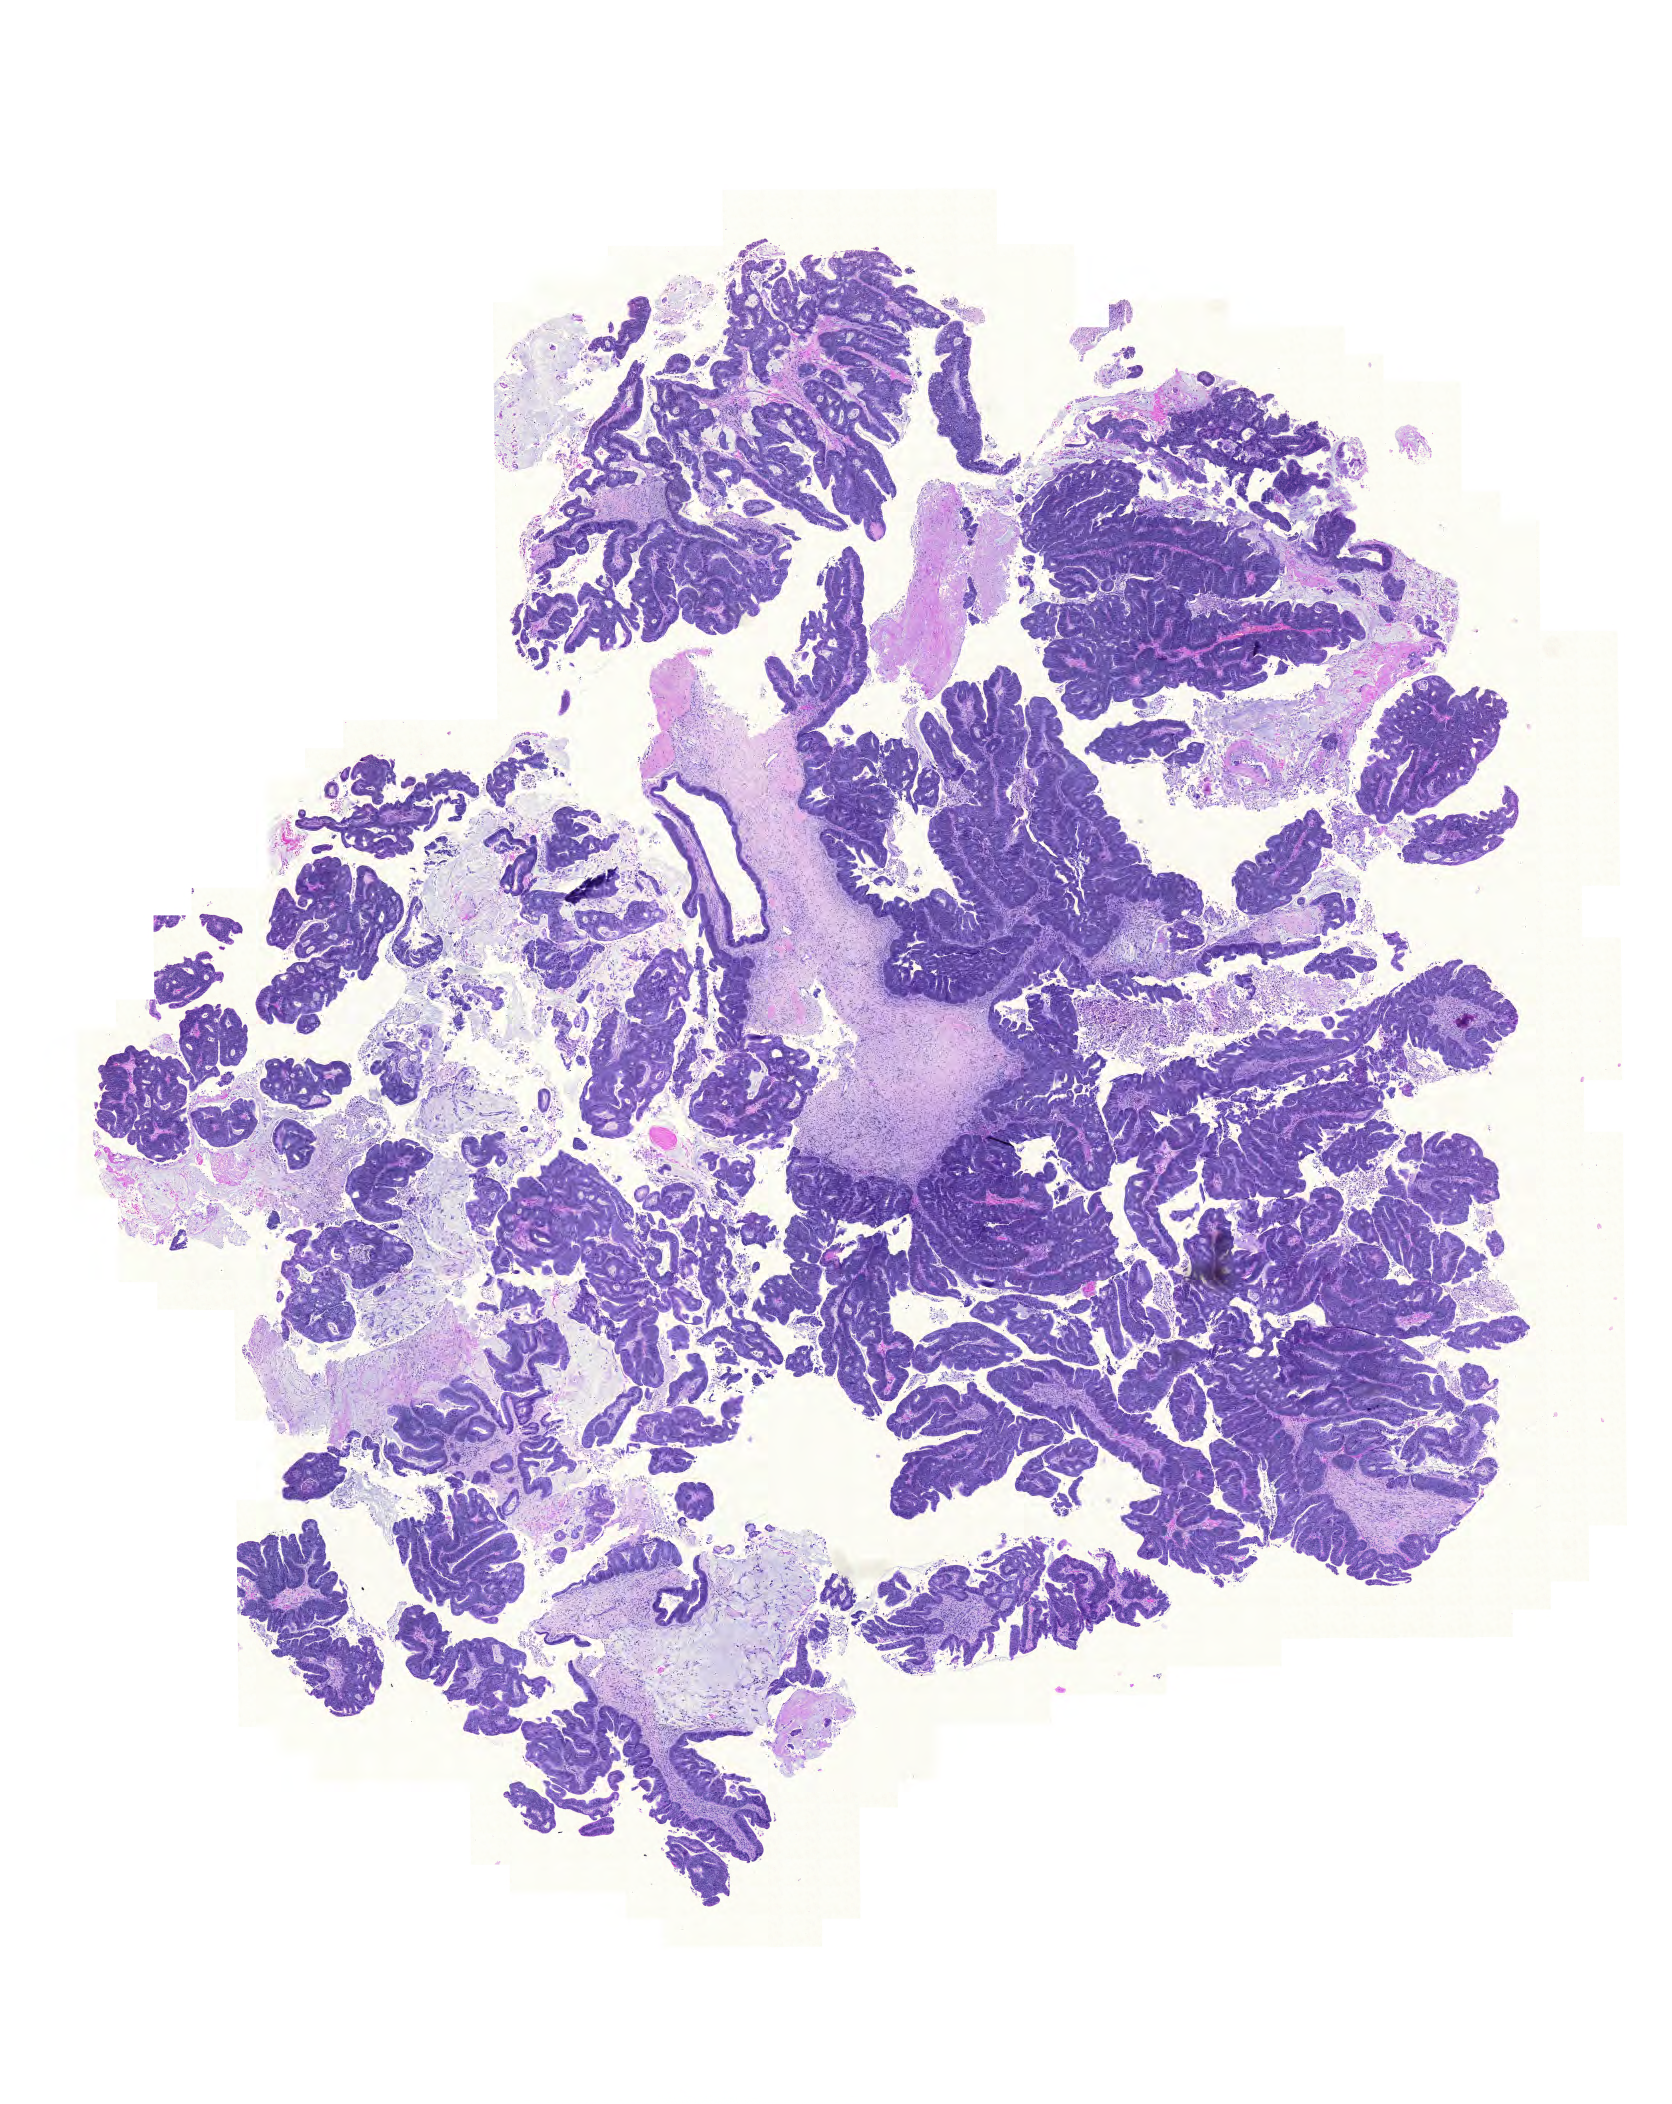
Whole-slide histology image, H&E — a low-resolution overview of the entire scanned area, about 12.4 x 15.7 mm, formalin-fixed paraffin-embedded (FFPE) diagnostic section, colon, primary tumour sample. Male, age 70 years at initial diagnosis.
AJCC pathologic stage: I (6th edition). Lymph nodes positive (case pathology): 0 of 46 examined. Diagnosis: Adenocarcinoma, NOS (sigmoid colon).